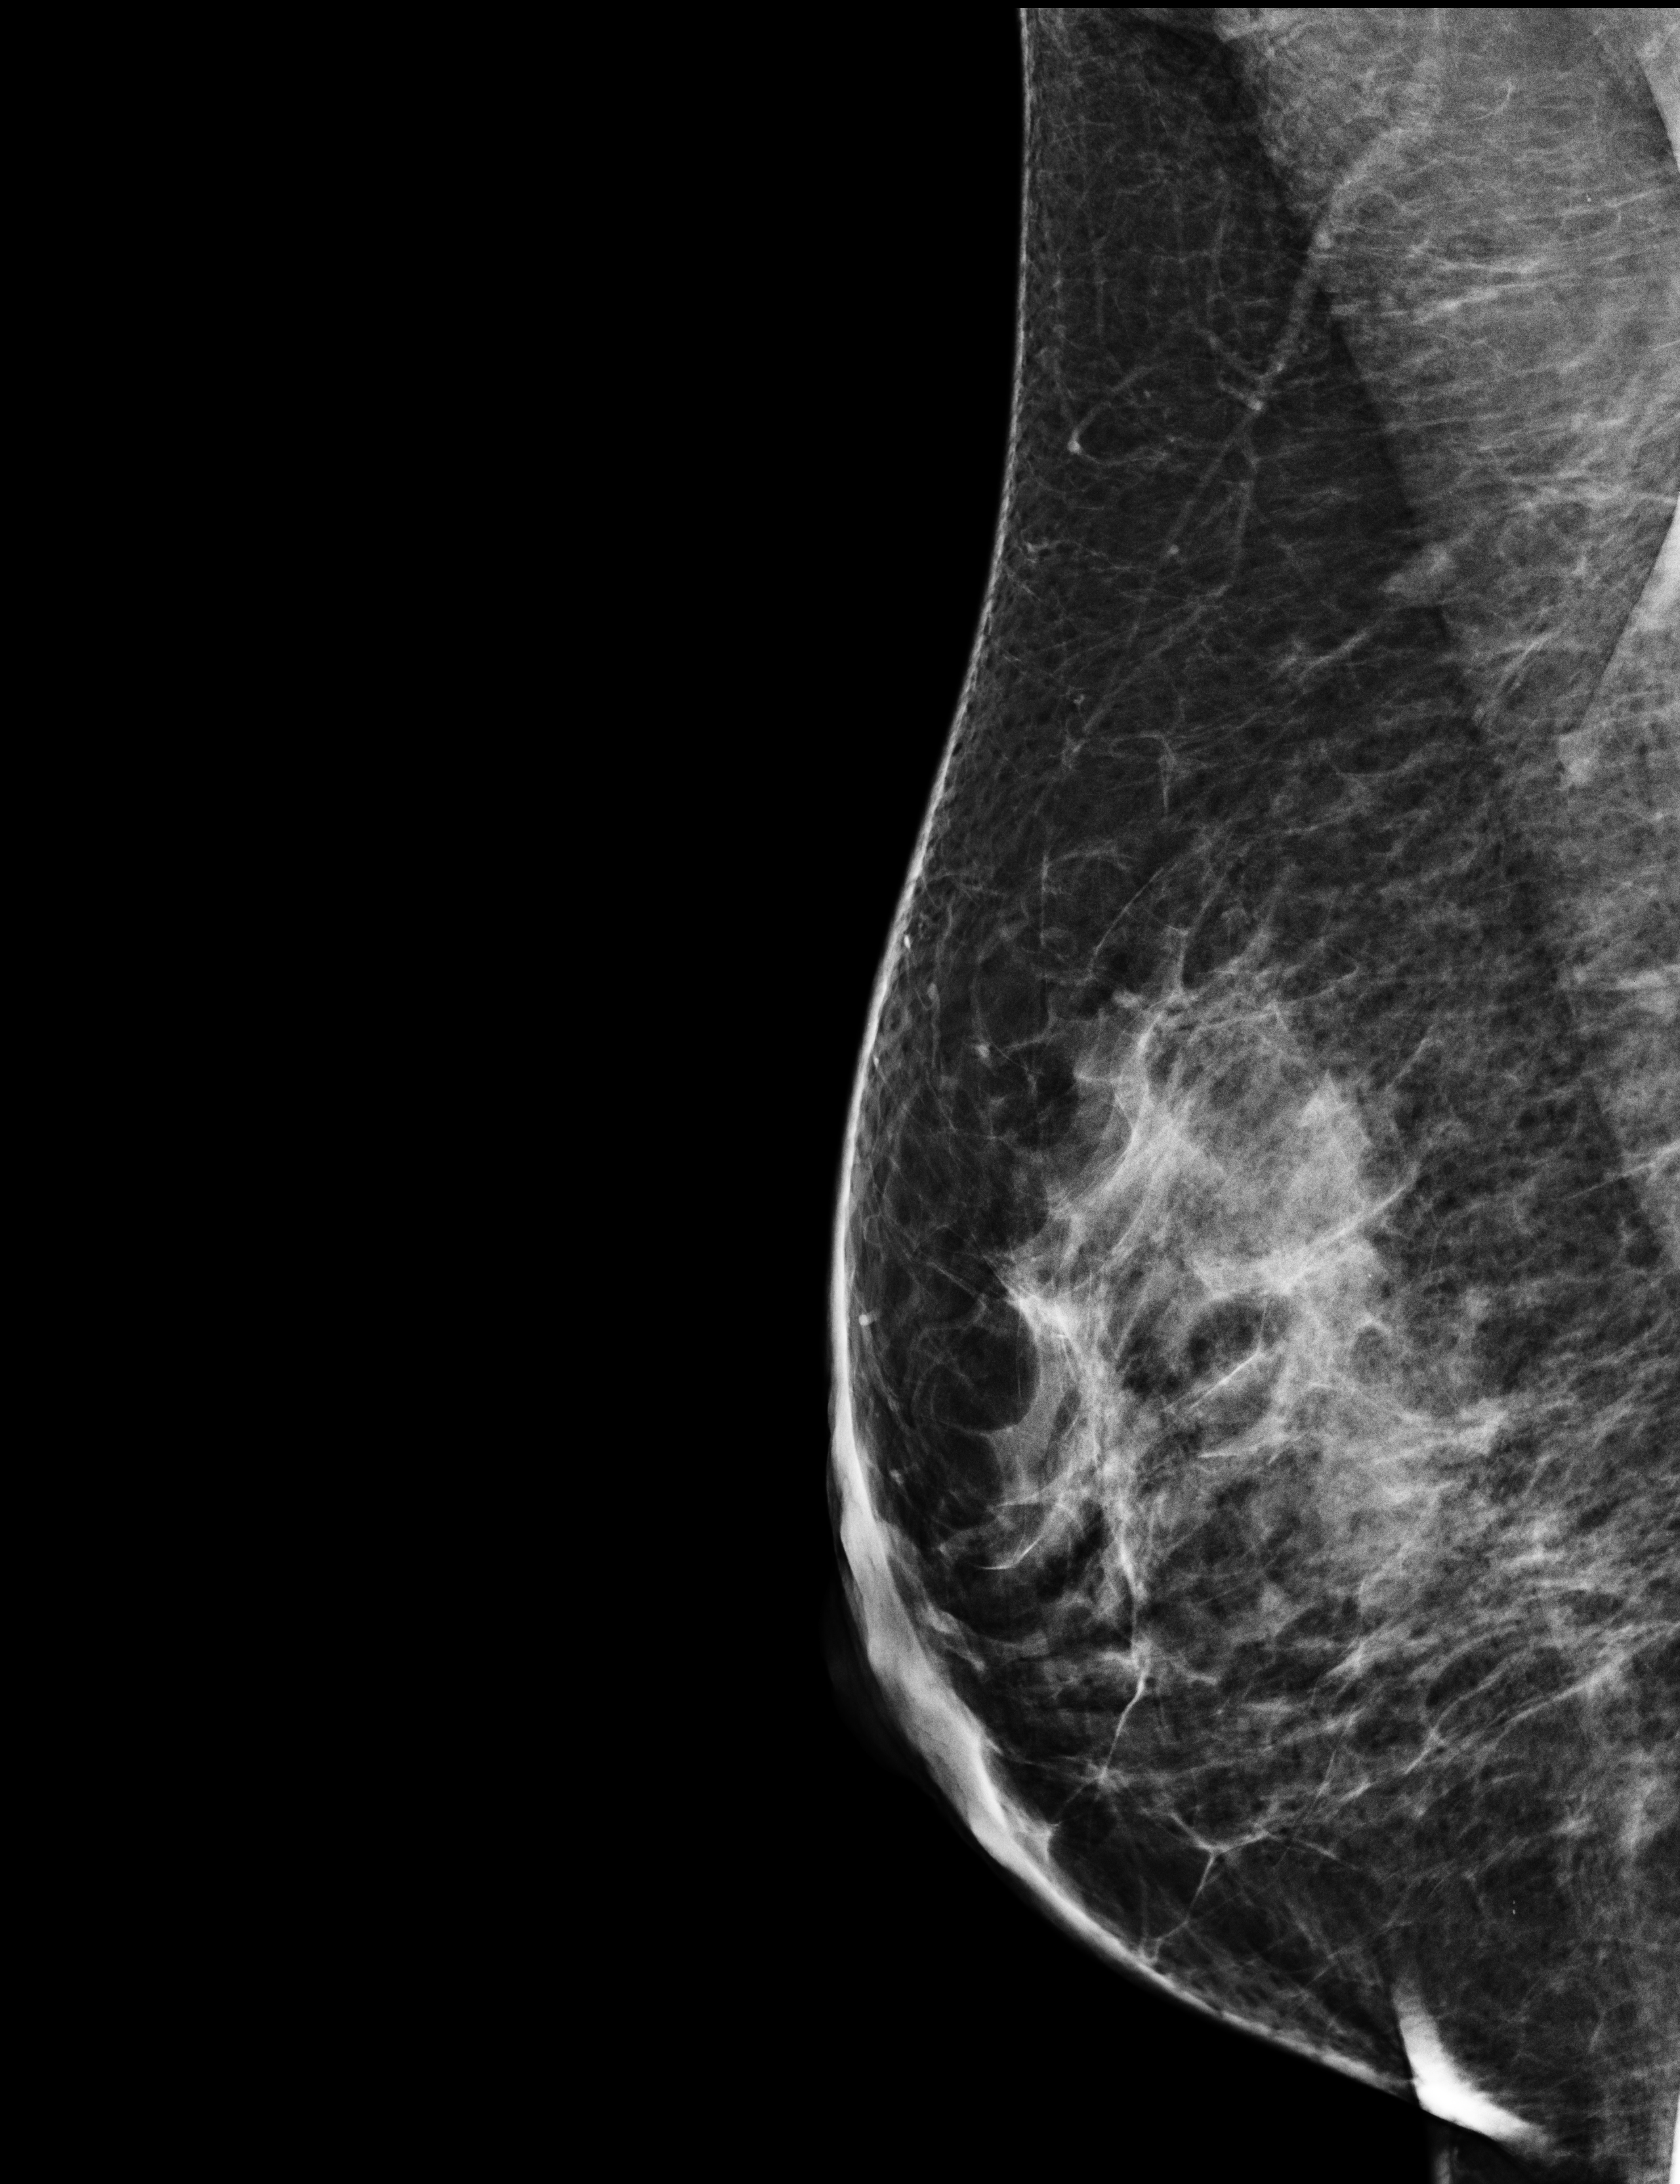
Screening examination, compressed breast thickness 53 mm. Female patient, age 46 years.
Image type: full-field digital mammogram. Breast: right. Projection: medio-lateral oblique projection. Breast density at the screening exam (both breasts): heterogeneously dense (BI-RADS density category c). Final BI-RADS assessment for this screening round (tomosynthesis exam, both breasts): category 2. Recall: no recall after this screen.